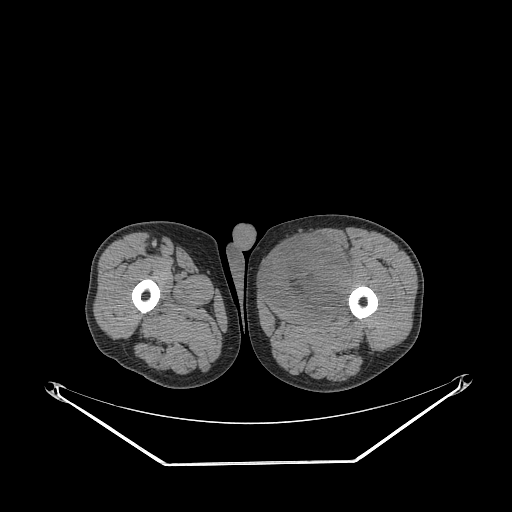
CT of an extremity soft-tissue mass (from a PET/CT study), one axial slice. Position 250 of 267 along the scan axis. Soft-tissue window (W 400 / L 40 HU). 3.75 mm slice thickness. 512 × 512 image matrix, field of view 500 × 500 mm. Male patient. From the clinical record (not read from this slice): histological type: pleiomorphic liposarcoma; grade: high; site of the primary tumour: left thigh.
Structures marked on this image (expert contour drawn on MRI and transferred to this co-registered scan by the dataset authors):
- gross tumour volume including surrounding oedema: box from (x=265, y=235) to (x=355, y=316) px
- gross tumour volume (mass): (x=265, y=235)–(x=352, y=316)